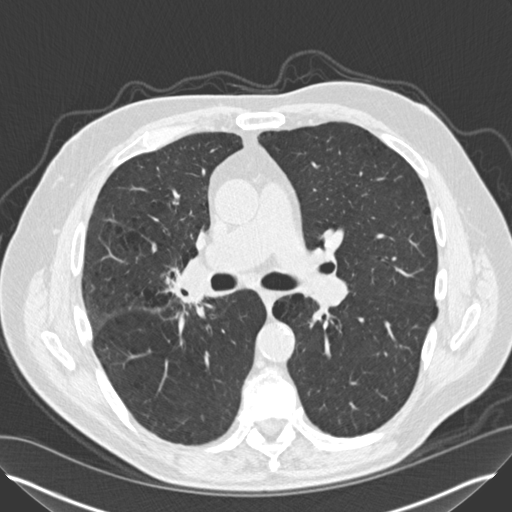
Low-dose screening chest CT, one axial slice. Slice 83 of 149 in the series (ordered by position). 120 kVp. Lung window (W 1500 / L -600 HU). 512 × 512 image matrix.
Outlined on this slice (manually delineated by an expert):
- lesion 2 (tumor, hilum of right lung): bounding box (x1, y1, x2, y2) in pixels: (182, 259, 207, 299)